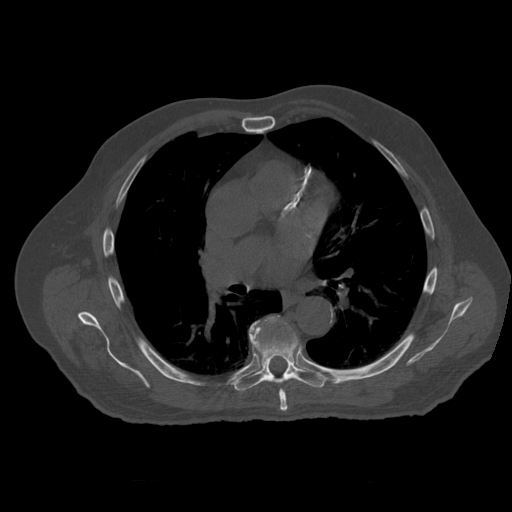
CT including the spine, one axial slice; reconstruction kernel STANDARD; bone window (W 1800 / L 400 HU); 512 × 512 image matrix, field of view 407 × 407 mm. Patient age 73 years. Case-level facts recorded for this patient, not image findings: primary cancer: prostate; vertebrae with lytic lesions (as recorded): L2.
Outlined on this slice (semi-automatic segmentation, software-assisted and operator-edited):
- T6 vertebra: bounding box <280,390,288,413> (left, top, right, bottom; pixels)
- T7 vertebra: <234,315,329,392>